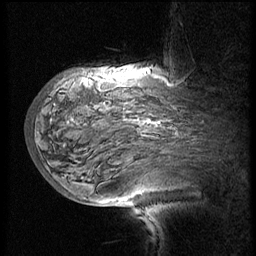
Breast MRI (dynamic contrast-enhanced), one sagittal slice; position 42 of 60 along the scan axis; 3 images stored at this slice position (order not interpretable as contrast timing); 1.5 T; TE 4.2 ms, TR 8.9 ms; 2.5 mm slice thickness; 256 × 256 image matrix, field of view 200 × 200 mm. Female patient, age 57 years. Case-level facts recorded for this patient, not image findings: setting: breast cancer imaged before/during neoadjuvant chemotherapy; receptor status: HER2-positive.
Outlined on this slice (semi-automatic segmentation, software-assisted and operator-edited):
- analysis volume of interest (the breast-tissue region the enhancement analysis was run in; not a lesion): box from (x=34, y=75) to (x=214, y=171) px
- tumour enhancement mask (voxels above the 140 % enhancement threshold inside the analysis volume of interest): (x=147, y=120)–(x=161, y=124)